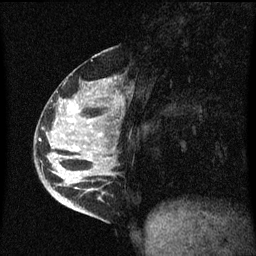
Breast MRI (dynamic contrast-enhanced), one sagittal slice; position 22 of 60 along the scan axis; dynamic contrast-enhanced series, image 2 of 3 at this slice position (ordered by acquisition); 1.5 T; TE 4.2 ms, TR 8.4 ms; 2 mm slice thickness; 256 × 256 image matrix, field of view 200 × 200 mm. Patient: female, 34 years. From the clinical record (not read from this slice): setting: breast cancer imaged before/during neoadjuvant chemotherapy; receptor status: HR-positive, HER2-negative.
Structures marked on this image (semi-automatic segmentation, software-assisted and operator-edited):
- analysis volume of interest (the breast-tissue region the enhancement analysis was run in; not a lesion): bounding box [x1, y1, x2, y2] px = [36, 52, 119, 215]
- tumour enhancement mask (voxels above the 70 % enhancement threshold inside the analysis volume of interest): [70, 120, 101, 135]